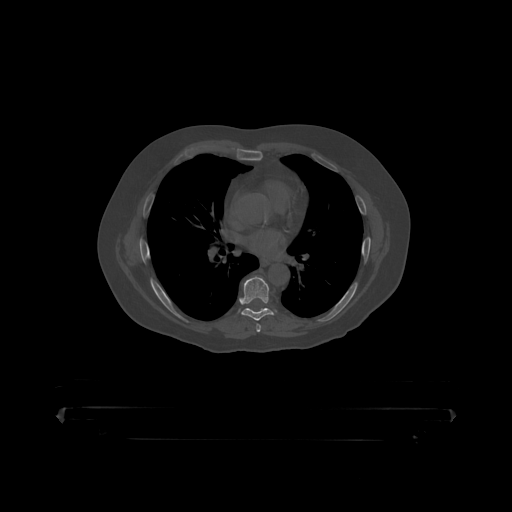
CT including the spine, one axial slice. Position 279 of 390 along the scan axis. 120 kVp. Bone window (W 1800 / L 400 HU). 1.25 mm slice thickness. 512 × 512 image matrix. Patient: male, 60 years. From the clinical record (not read from this slice): primary cancer: prostate.
Outlined on this slice (semi-automatically segmented with operator editing):
- T7 vertebra: bounding box <241,277,278,319> (left, top, right, bottom; pixels)